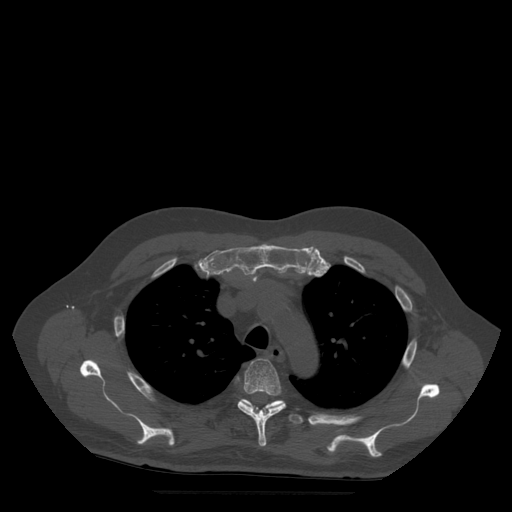
CT including the spine, one axial slice; position 387 of 522 along the scan axis; bone window (W 1800 / L 400 HU); 1.25 mm slice thickness; 512 × 512 image matrix. Patient age 72 years. Case-level facts recorded for this patient, not image findings: primary cancer: prostate.
Structures marked on this image (semi-automatic segmentation, software-assisted and operator-edited):
- T4 vertebra: bounding box [x1, y1, x2, y2] px = [238, 359, 286, 447]
- T5 vertebra: [239, 400, 315, 425]